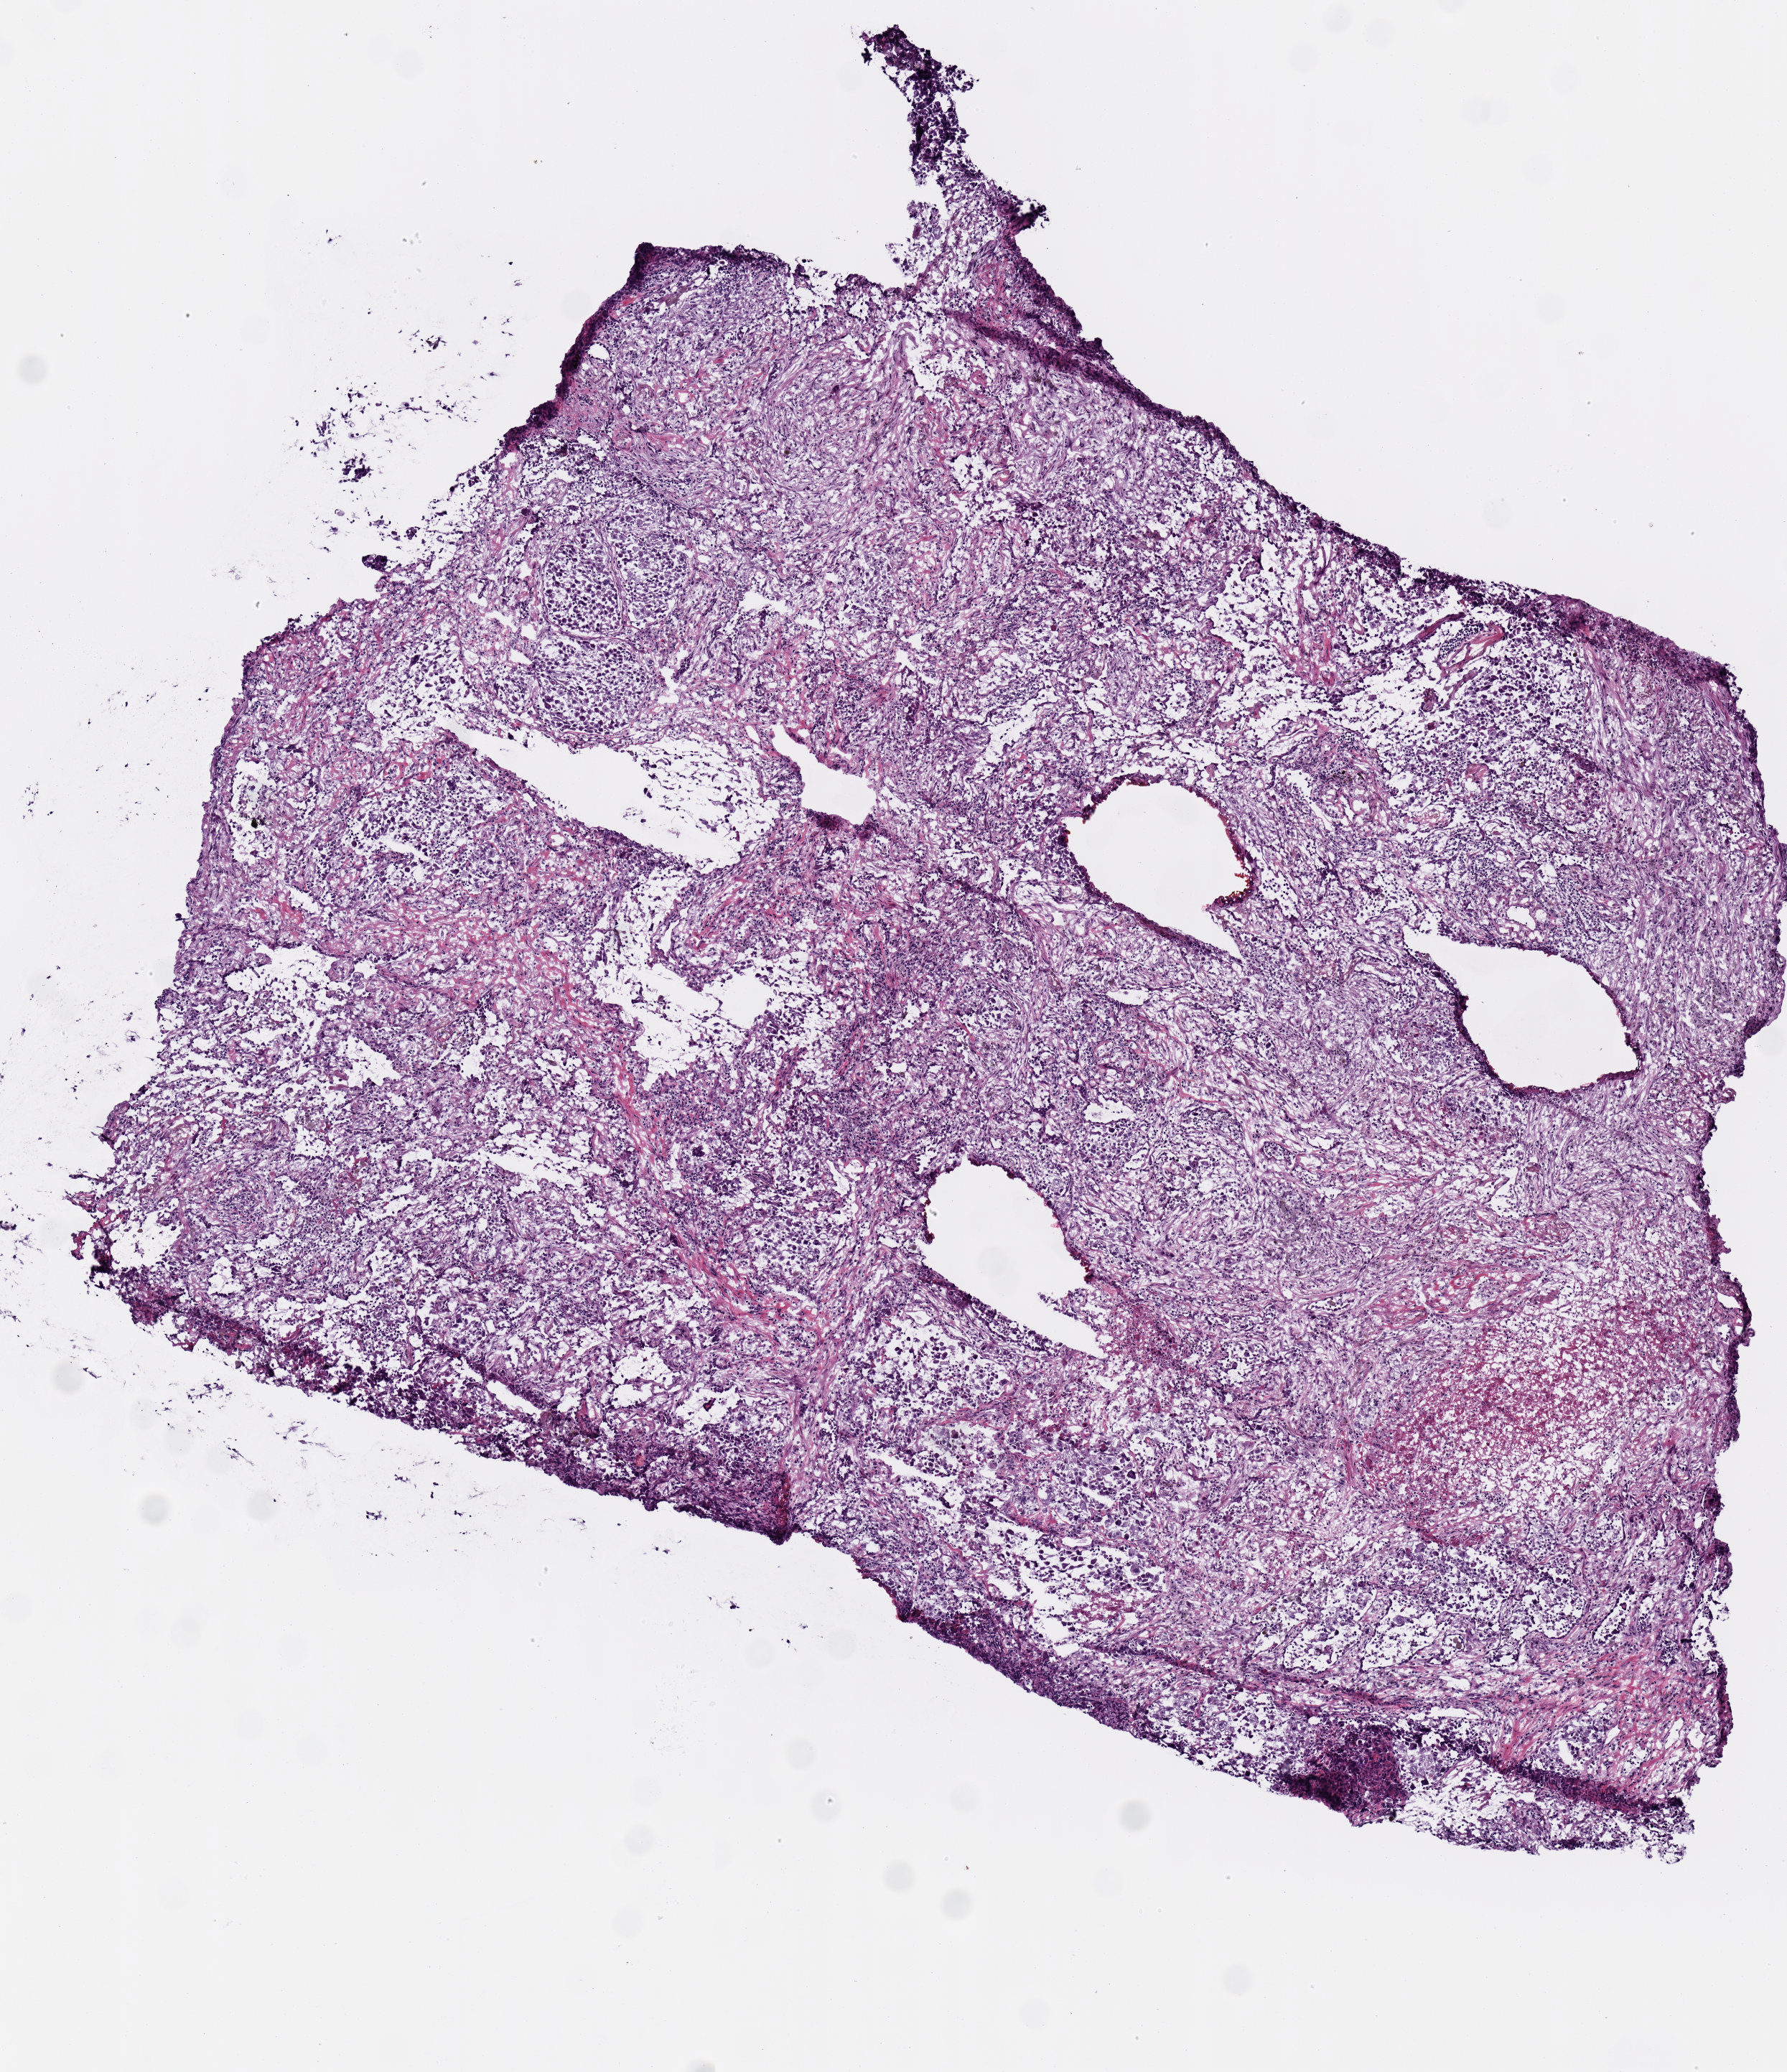
H&E-stained whole-slide image — whole scanned area (about 4.9 x 5.7 mm, acquisition: 20x scan) shown as a low-resolution overview. Frozen section. Lung, primary tumour sample. Female, age 61 years at initial diagnosis. Composition of this section per pathologist review: tumour cells 85%, tumour nuclei 65%, normal cells 0%, stromal cells 15%, necrosis 0%.
Pathologic diagnosis: Adenocarcinoma, NOS (upper lobe, lung). AJCC pathologic stage: IA.